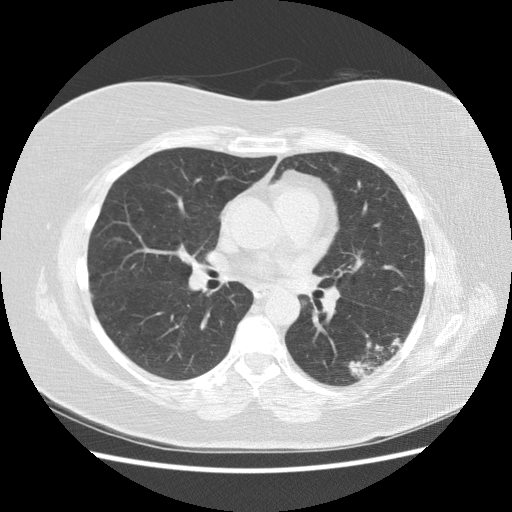
Low-dose screening chest CT, axial slice. Third screening round (two years after baseline). Lung window (W 1500 / L -600 HU). 2.5 mm slice thickness. Slice 82 of 151 in the series. 512 × 512 image matrix, field of view 360 × 360 mm. Female participant, aged 57 years at enrolment. Current smoker at enrolment.
- Expert-annotated lung lesion, bounding box [x1, y1, x2, y2] px = [333, 325, 410, 388].
- The exam's reader record, not a measurement of the box and not confirmed to be the same lesion: non-calcified nodule or mass ≥4 mm, left lower lobe, 40 × 20 mm, poorly defined margins, mixed attenuation, pre-existing on the prior screen: yes; interval growth: yes.
- Official screen result: positive, other.
- Lung cancer was diagnosed 55 days after this screen: squamous cell carcinoma, NOS, left lower lobe, poorly differentiated (G3), stage IB (AJCC 6th edition), 40 mm at pathology.